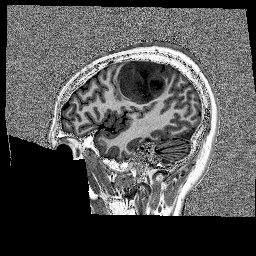
Brain MRI from a brain-tumour surgery series, one sagittal slice. Slice 46 of 176 in the series (ordered by position). 1 mm slice thickness. 256 × 256 image matrix, field of view 256 × 256 mm. Case-level facts recorded for this patient, not image findings: histopathology: Glioblastoma; WHO grade: 4; IDH mutation: no; tumour location: Left Frontal.
Annotated regions visible in this slice (outlined manually by an expert reader):
- tumour: bounding box <118,58,175,103> (left, top, right, bottom; pixels)